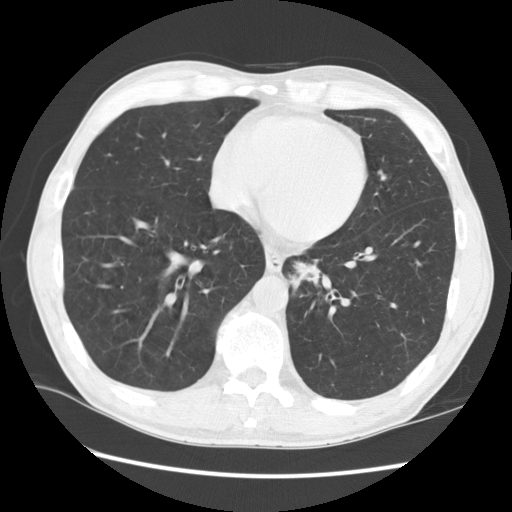
Low-dose screening chest CT, one axial slice. Position 46 of 141 along the scan axis. Reconstruction kernel STANDARD. 120 kVp. Lung window (W 1500 / L -600 HU). 2.5 mm slice thickness. 512 × 512 image matrix.
Structures marked on this image (expert manual segmentation):
- lesion 2 (nodule, lower lobe of left lung): bounding box <293,261,318,286> (left, top, right, bottom; pixels)